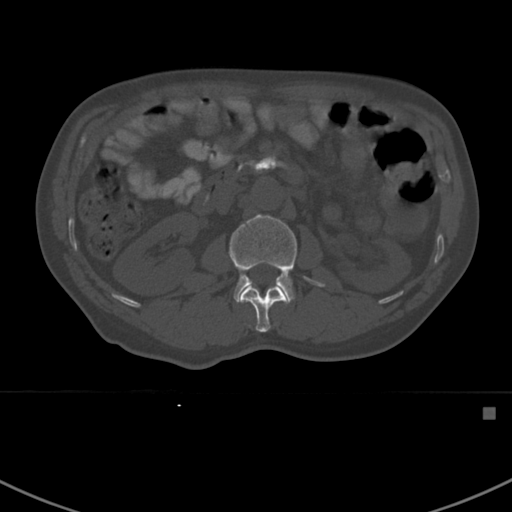
CT including the spine, one axial slice. Slice 296 of 412 in the series (ordered by position). 120 kVp. Bone window (W 1800 / L 400 HU). 1.5 mm slice thickness. 512 × 512 image matrix, field of view 358 × 358 mm. Patient: male, 59 years. Case-level facts recorded for this patient, not image findings: primary cancer: prostate.
Annotated regions visible in this slice (semi-automatic segmentation, software-assisted and operator-edited):
- L1 vertebra: bounding box <240,286,287,332> (left, top, right, bottom; pixels)
- L2 vertebra: <229,214,325,304>